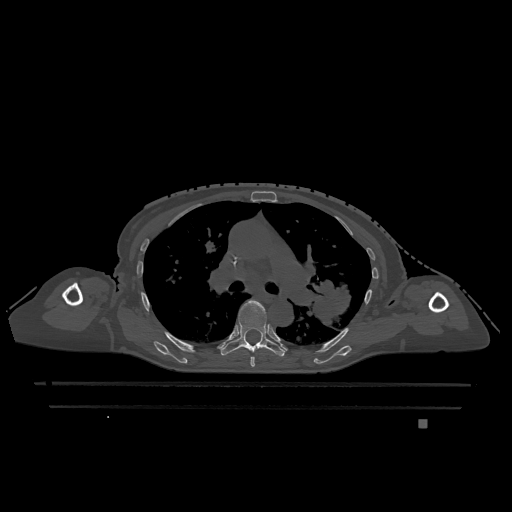
CT including the spine, one axial slice. Position 802 of 1317 along the scan axis. Bone window (W 1800 / L 400 HU). 0.5 mm slice thickness. 512 × 512 image matrix, field of view 500 × 500 mm. Patient: female, 74 years. Case-level facts recorded for this patient, not image findings: primary cancer: lung.
Outlined on this slice (semi-automatic segmentation, software-assisted and operator-edited):
- T5 vertebra: box from (x=250, y=356) to (x=255, y=367) px
- T6 vertebra: (x=220, y=300)–(x=285, y=357)